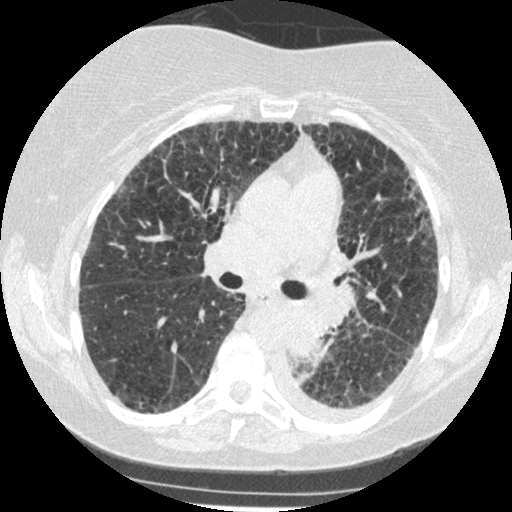
Low-dose screening chest CT, axial slice, third screening round (two years after baseline), lung window (W 1500 / L -600 HU). Female, age 60 years at enrolment.
Lesion marked by an expert reader, bounding box [x1, y1, x2, y2] px = [269, 308, 341, 373]. The exam's reader record, not a measurement of the box and not confirmed to be the same lesion: non-calcified nodule or mass ≥4 mm, left lower lobe, 54 × 38 mm, smooth margins, soft tissue attenuation, pre-existing on the prior screen: yes; interval growth: yes. Official screen result: positive, other.